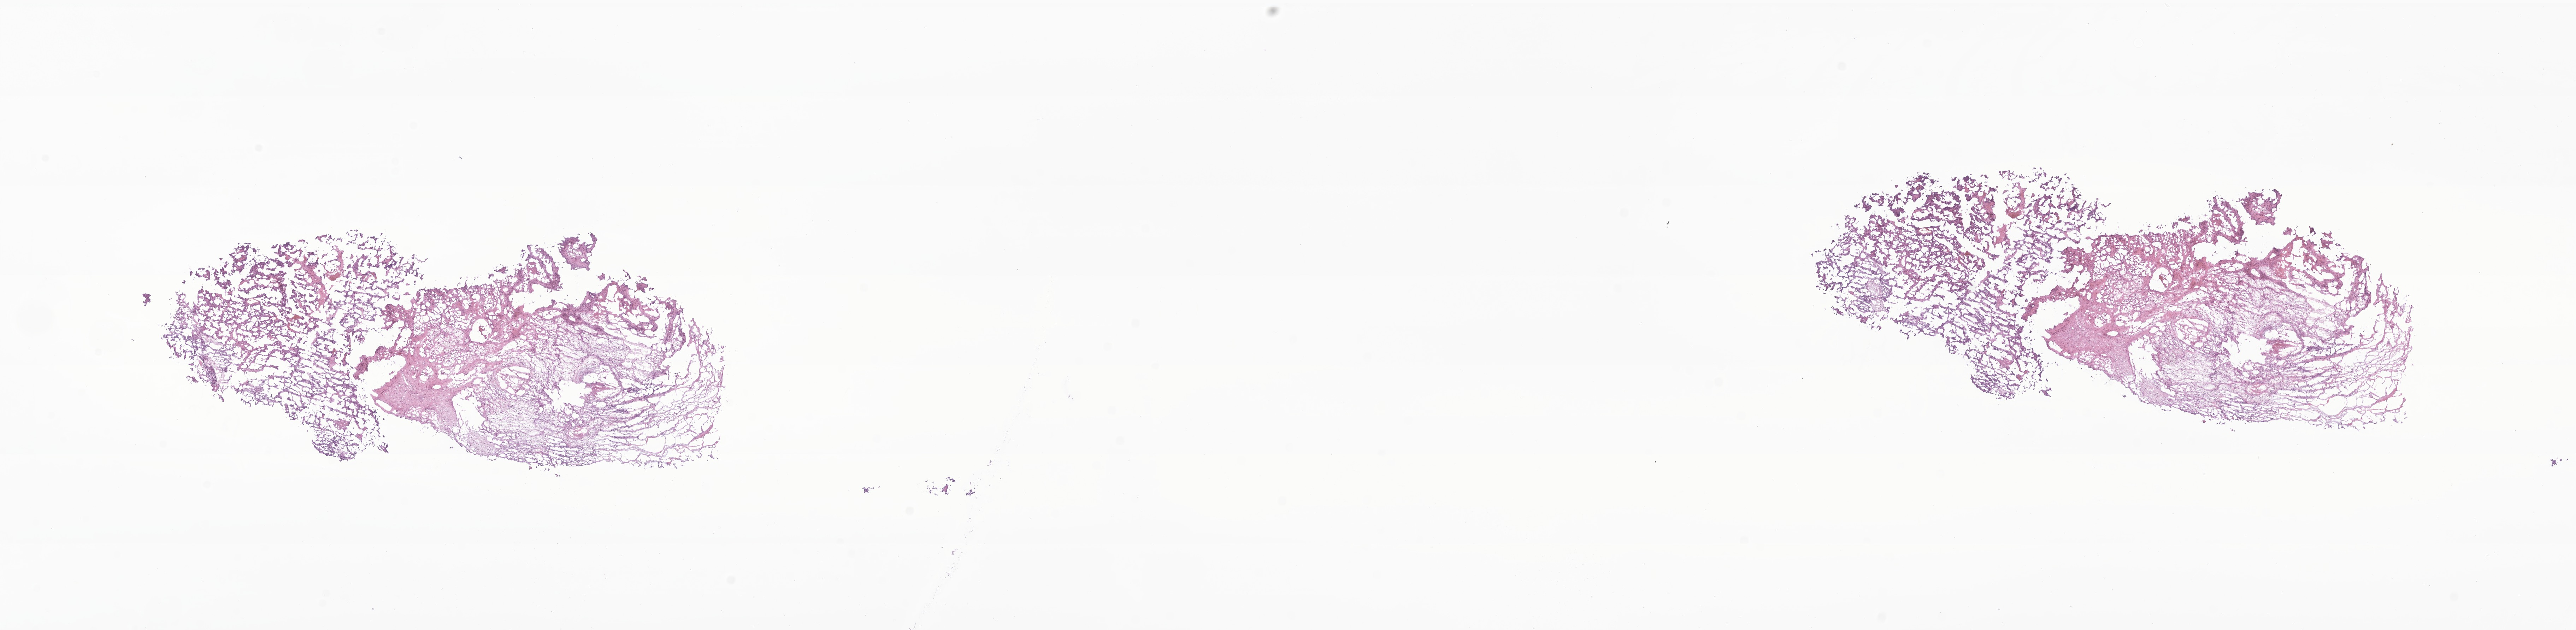
Hematoxylin and eosin (H&E) whole-slide image of tumor tissue from the brain, a low-resolution overview of the entire scanned area, about 30.7 x 7.5 mm. Frozen section (OCT-embedded). Male patient, age 57 months (4 years 9 months).
Diagnosis (ICD-O-3 morphology term): Choroid plexus carcinoma.